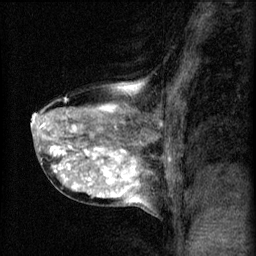
Breast MRI (dynamic contrast-enhanced), one sagittal slice. Position 32 of 60 along the scan axis. 3 images stored at this slice position (order not interpretable as contrast timing). 1.5 T. TE 4.2 ms, TR 8.2 ms. 2 mm slice thickness. 256 × 256 image matrix. Patient: female, 40 years.
Structures marked on this image (semi-automatically segmented with operator editing):
- analysis volume of interest (the breast-tissue region the enhancement analysis was run in; not a lesion): box from (x=31, y=80) to (x=167, y=211) px
- tumour enhancement mask (voxels above the 70 % enhancement threshold inside the analysis volume of interest): (x=32, y=84)–(x=141, y=199)